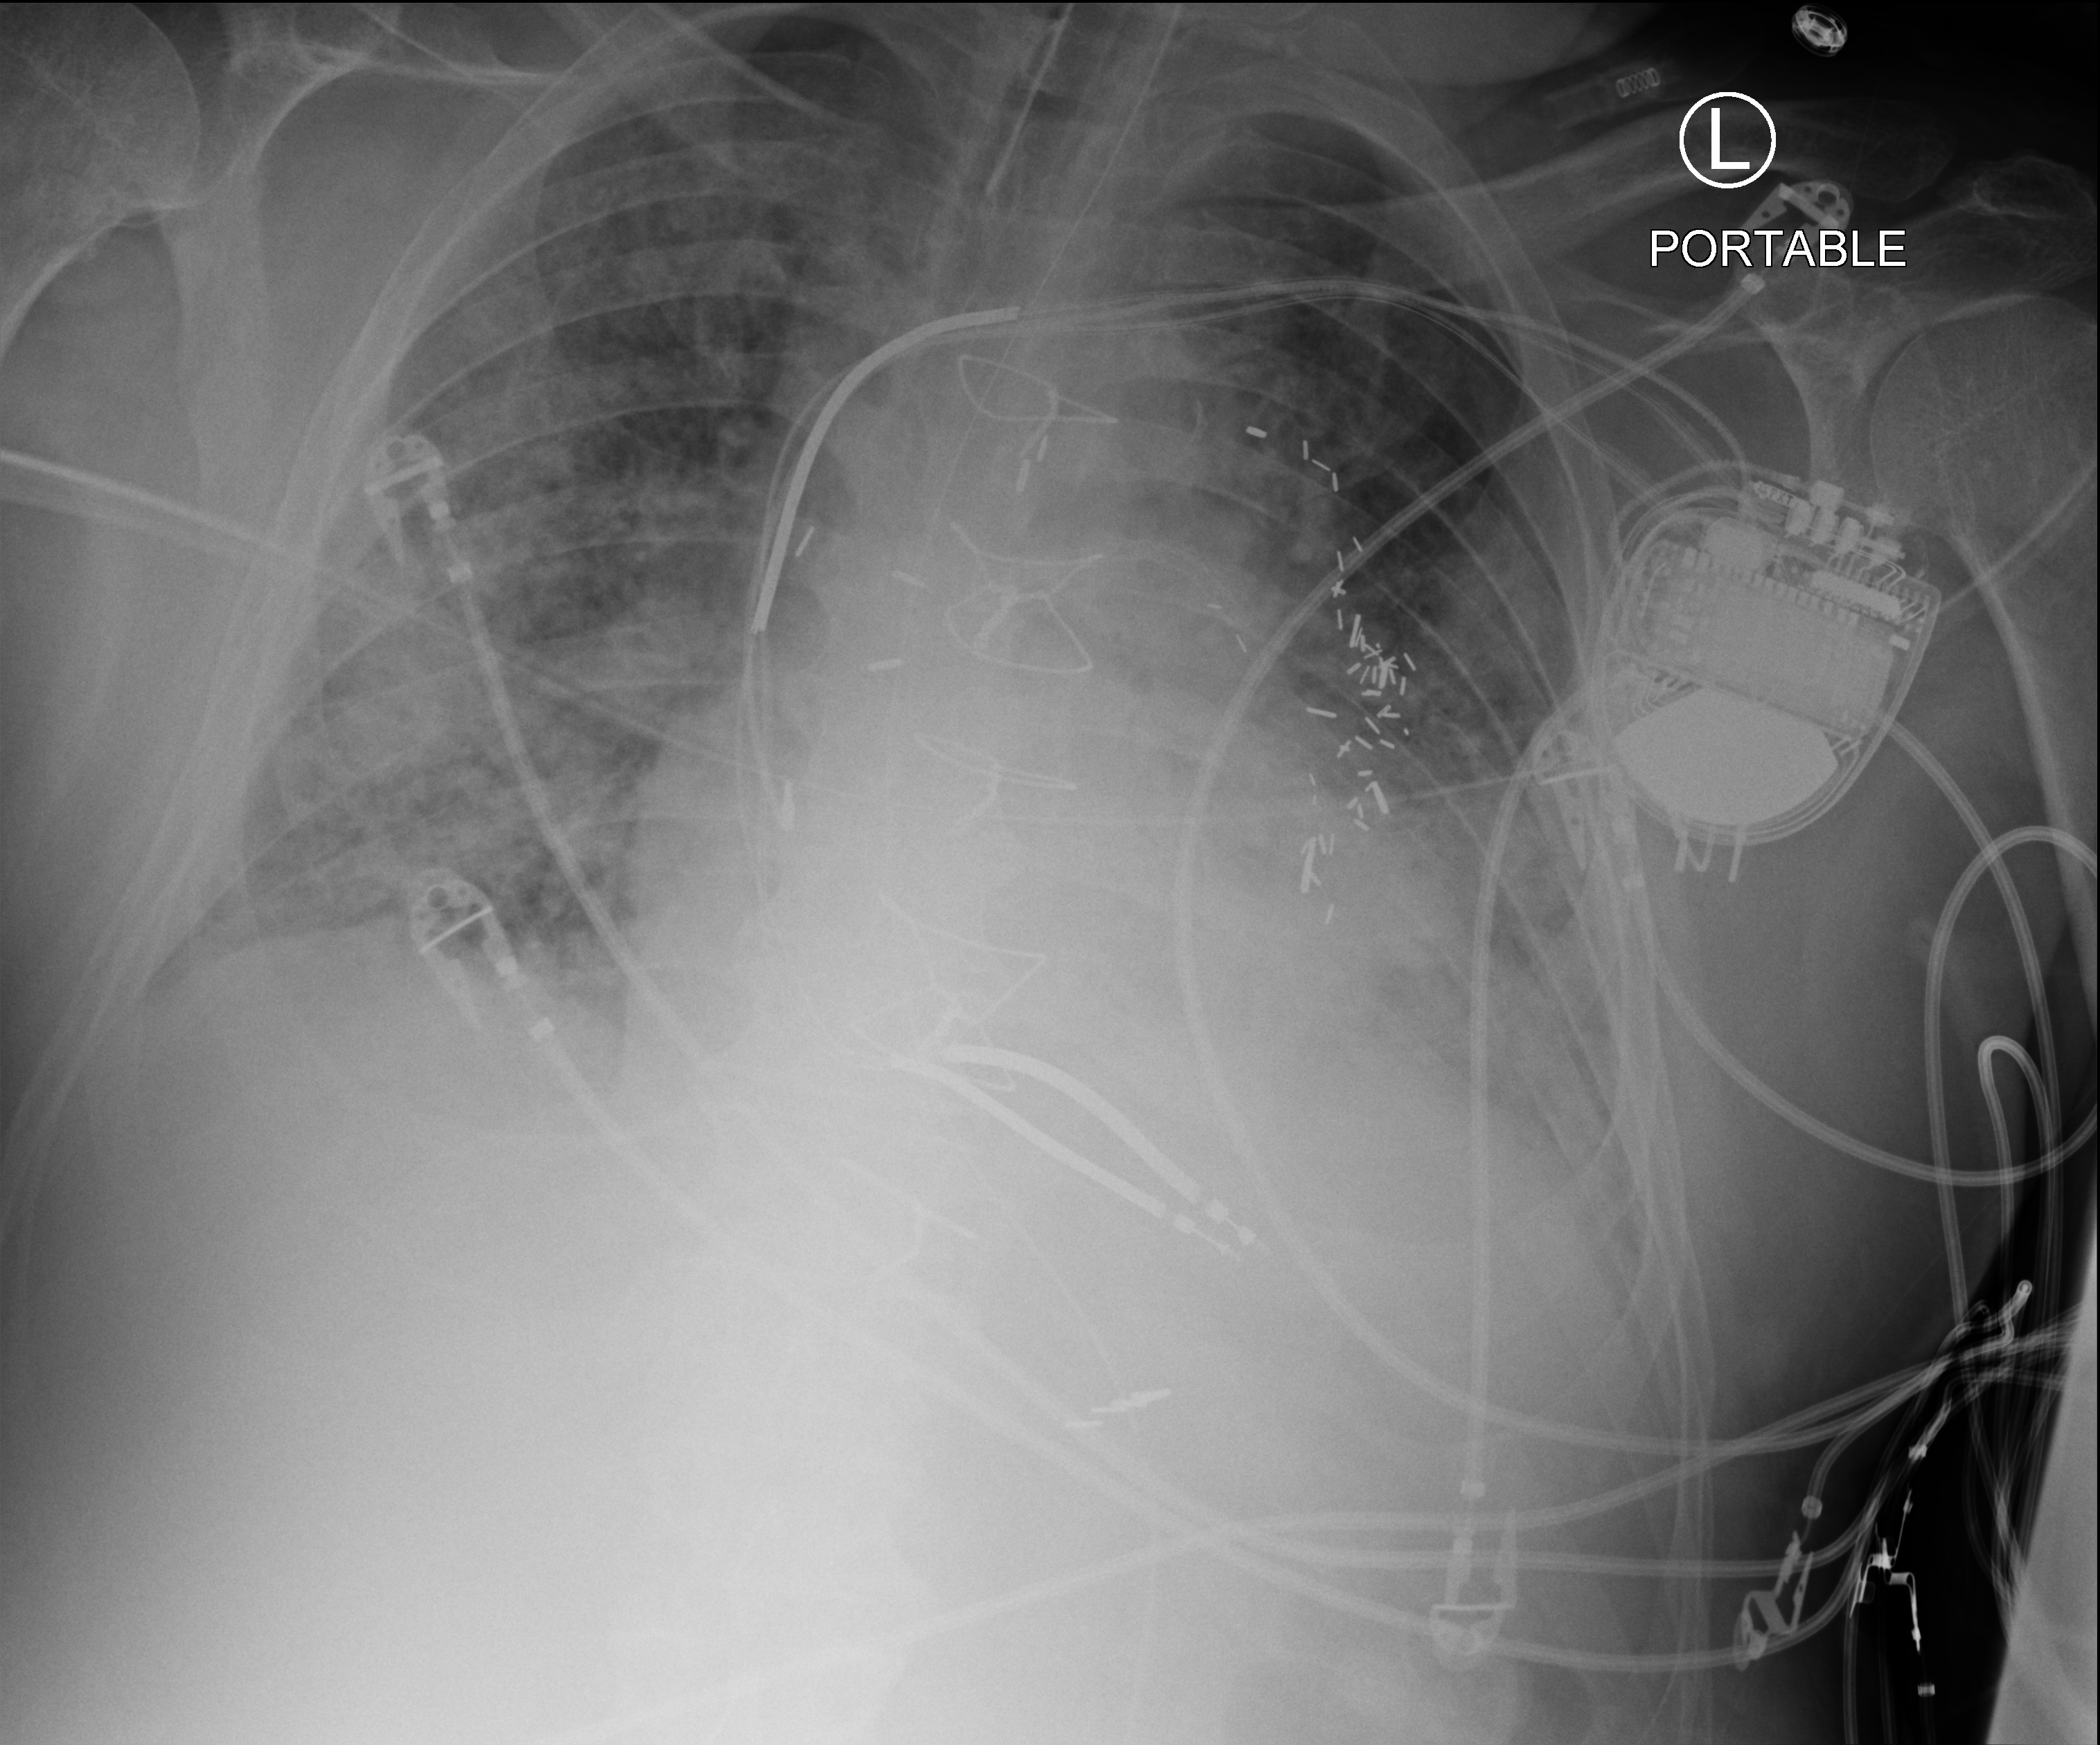
Chest X-ray (portable), anteroposterior (AP) projection. Male patient hospitalised with COVID-19, age 60–74 years.
Admission-level facts for this patient (not findings on this image; timing relative to this image not recorded): mechanically ventilated during this hospital stay: yes; admitted to intensive care during this hospital stay: yes.